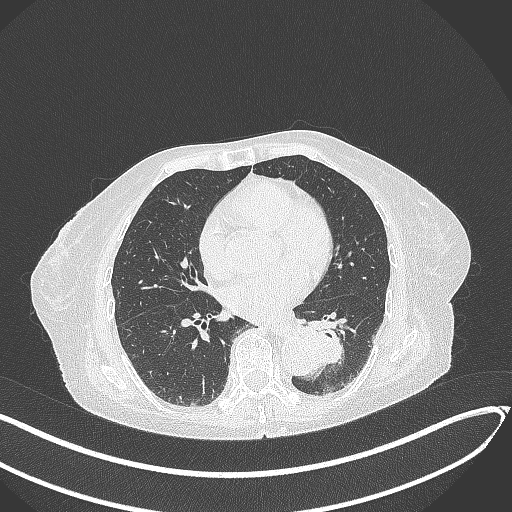
Chest CT, one axial slice; position 107 of 324 along the scan axis; lung window (W 1500 / L -600 HU); 1 mm slice thickness; 512 × 512 image matrix, field of view 400 × 400 mm. Female patient, age 82 years. Case-level facts recorded for this patient, not image findings: clinical TNM (as recorded): T1b N0 M1.
Annotated regions visible in this slice (rectangle marked by the reading radiologist):
- lung tumour (recorded histology: adenocarcinoma): bounding box <294,316,349,369> (left, top, right, bottom; pixels)